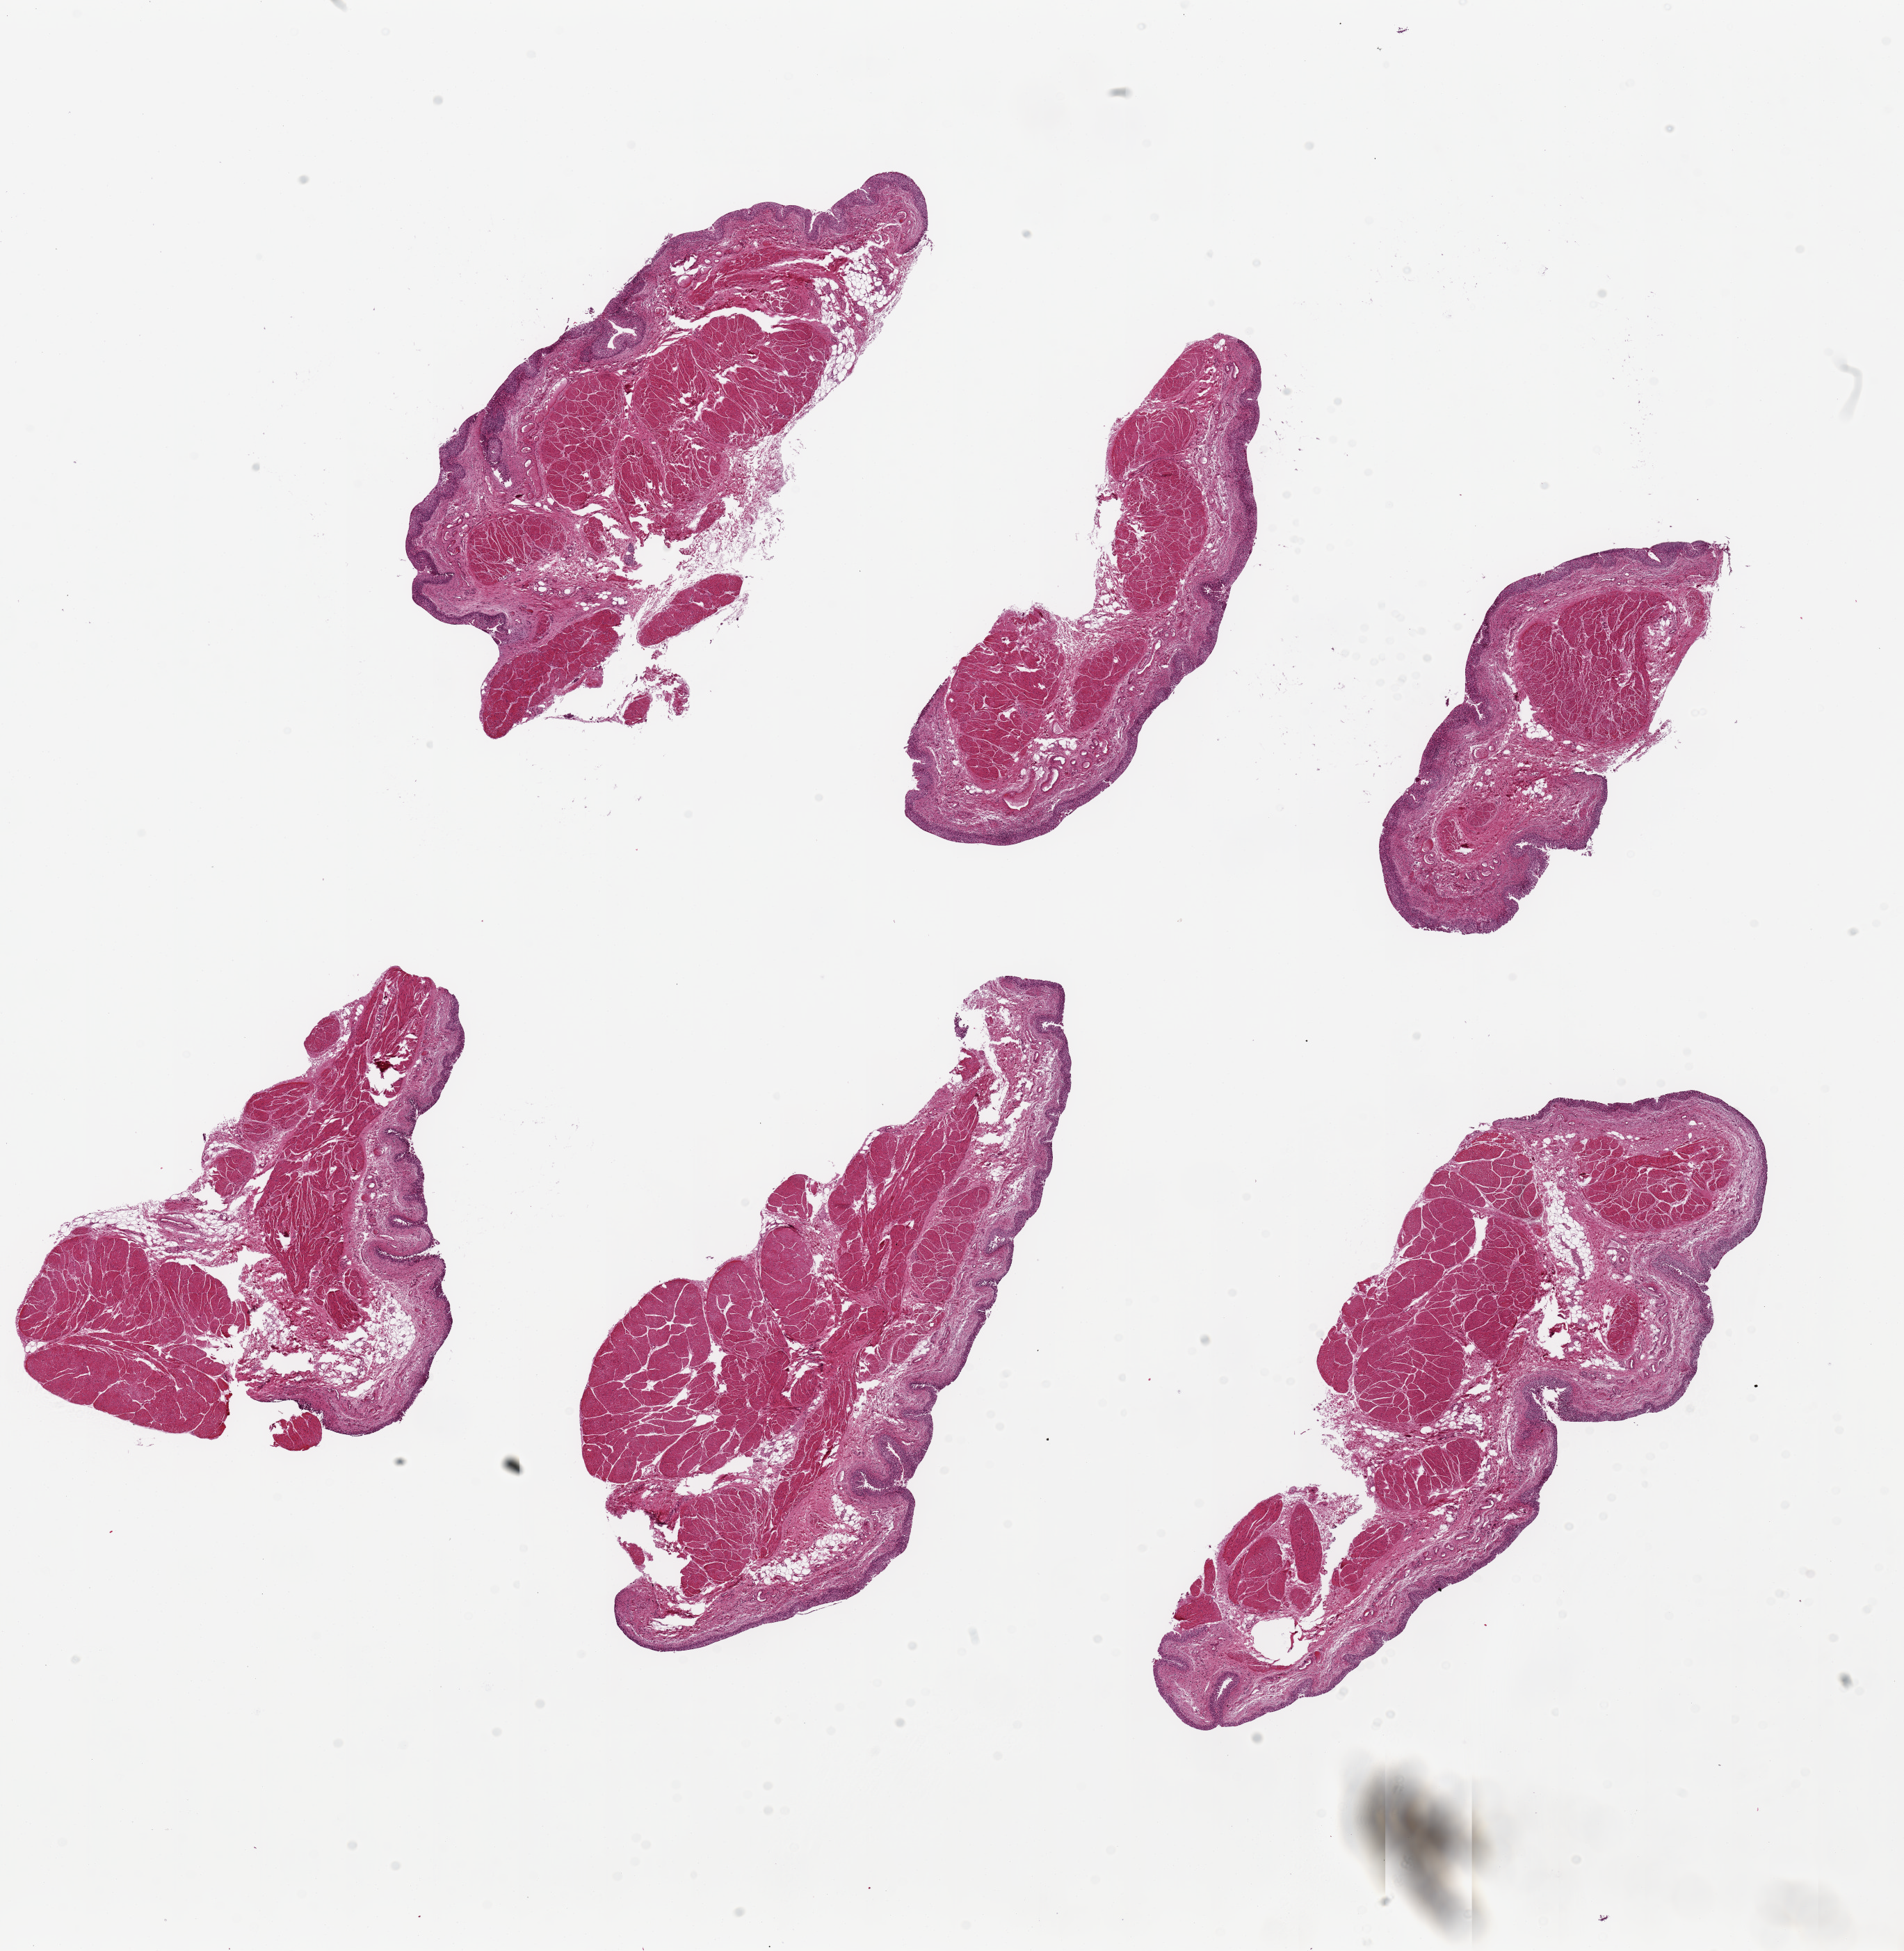
Whole-slide image, haematoxylin and eosin stain, whole scanned area (about 21.7 x 22.2 mm) shown as a low-resolution overview, PAXgene-fixed, paraffin-embedded tissue, sampled site (target tissue): urinary bladder, tissue donor sample. Male donor.
Reviewer comment on this tissue sample: 6 pieces up to 9.3x4.5 mm; little epithelial sloughing.